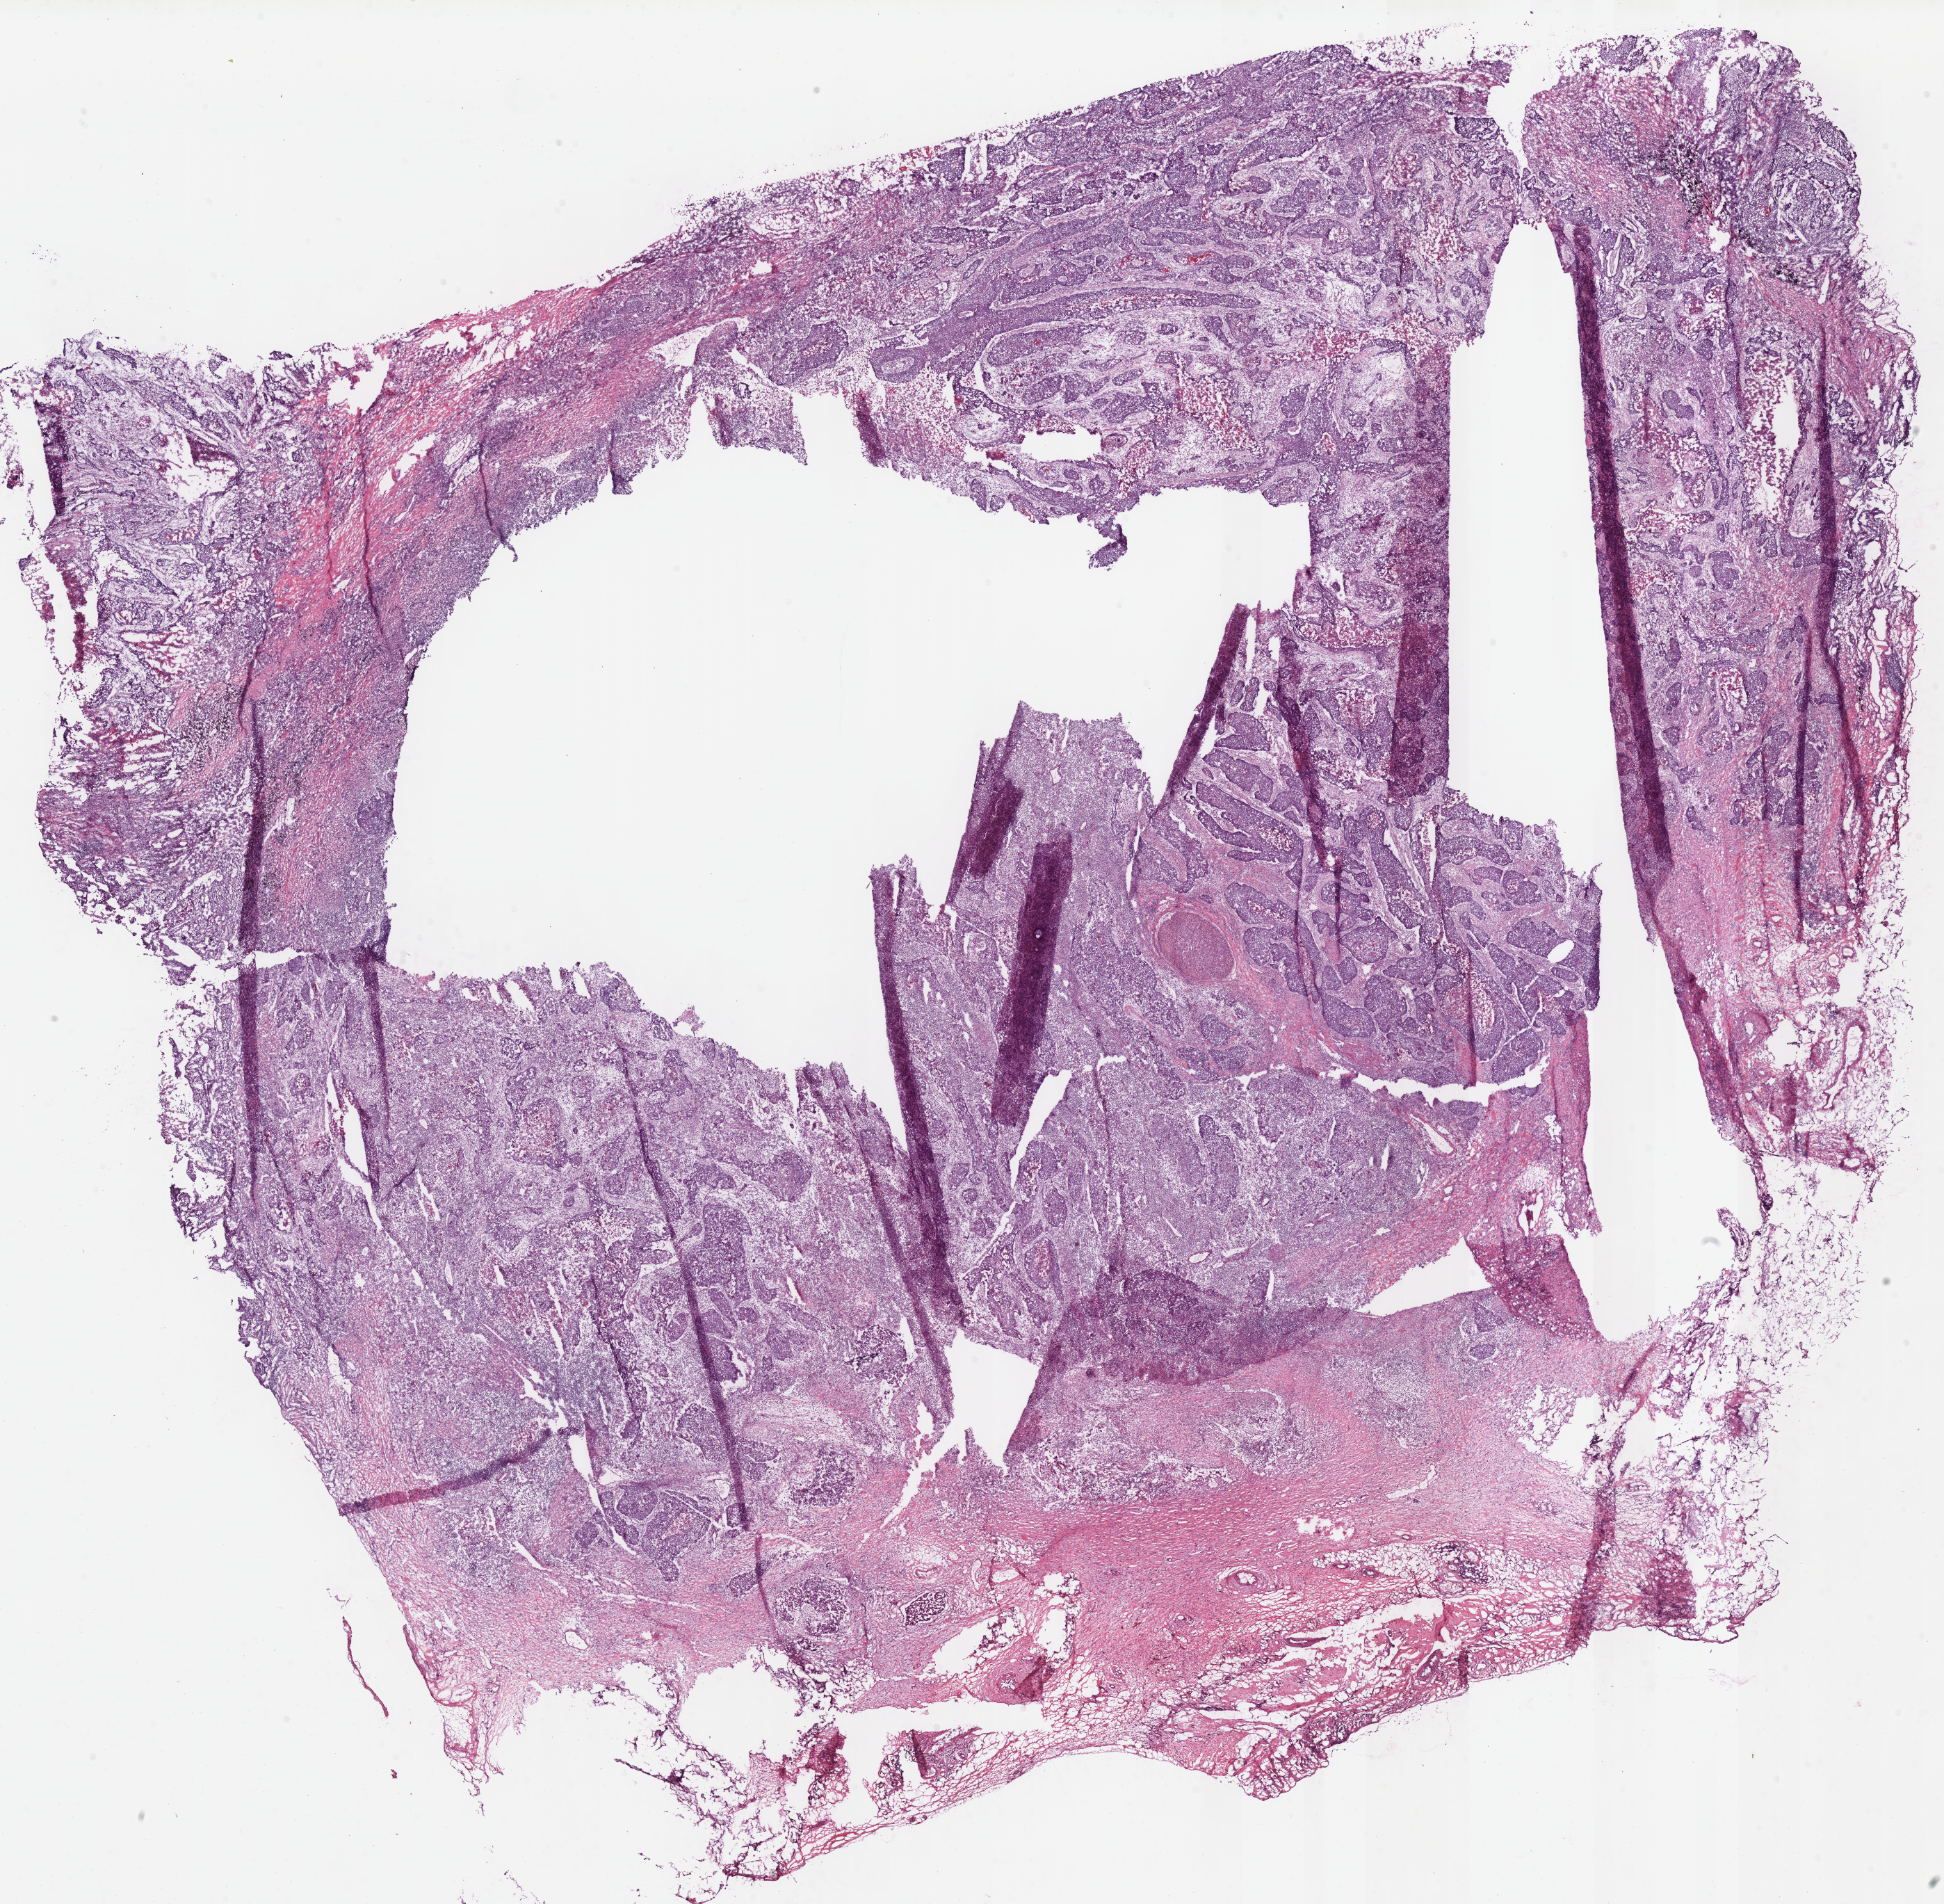
Whole-slide histology image, H&E — whole scanned area (about 22.0 x 21.6 mm) shown as a low-resolution overview; frozen section; lung, primary tumour sample. Patient: male, age at initial diagnosis 65 years. Slide review estimates, as recorded: tumour cells 88%, tumour nuclei 50%, normal cells 12%, stromal cells 0%, necrosis 0%. Inflammatory infiltration, as recorded: lymphocyte infiltration 15%, monocyte infiltration 0%, neutrophil infiltration 35%.
AJCC pathologic stage: IB (7th edition). Pathologic diagnosis: Squamous cell carcinoma, NOS (upper lobe, lung). Laterality: left.